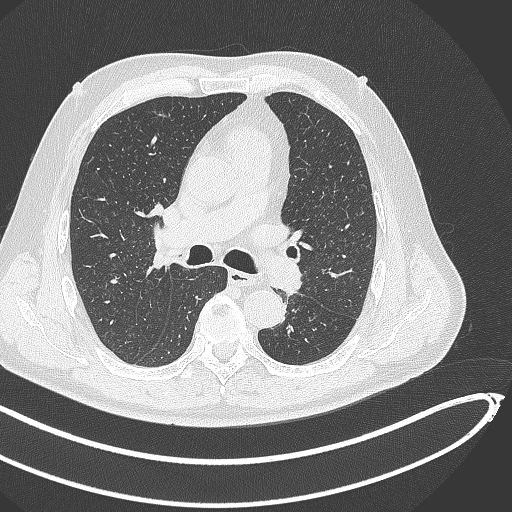
Chest CT, one axial slice; position 281 of 468 along the scan axis; 120 kVp; lung window (W 1500 / L -600 HU); 512 × 512 image matrix, field of view 400 × 400 mm. Male patient, age 64 years. From the clinical record (not read from this slice): clinical TNM (as recorded): T1c N0 M0; histopathological grade: G2.
Annotated regions visible in this slice (rectangle marked by the reading radiologist):
- lung tumour (recorded histology: squamous cell carcinoma): box from (x=262, y=246) to (x=309, y=296) px